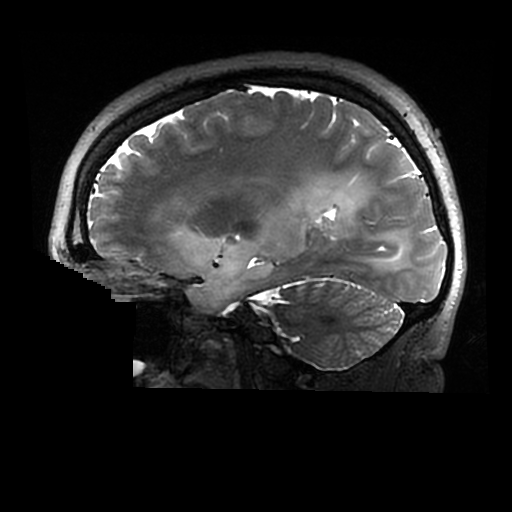
Brain MRI from a brain-tumour surgery series, one sagittal slice; 512 × 512 image matrix, field of view 240 × 240 mm. From the clinical record (not read from this slice): histopathology: Astrocytoma; WHO grade: 2; IDH mutation: yes.
Structures marked on this image (manually delineated by an expert):
- tumour: bounding box <173,180,407,310> (left, top, right, bottom; pixels)